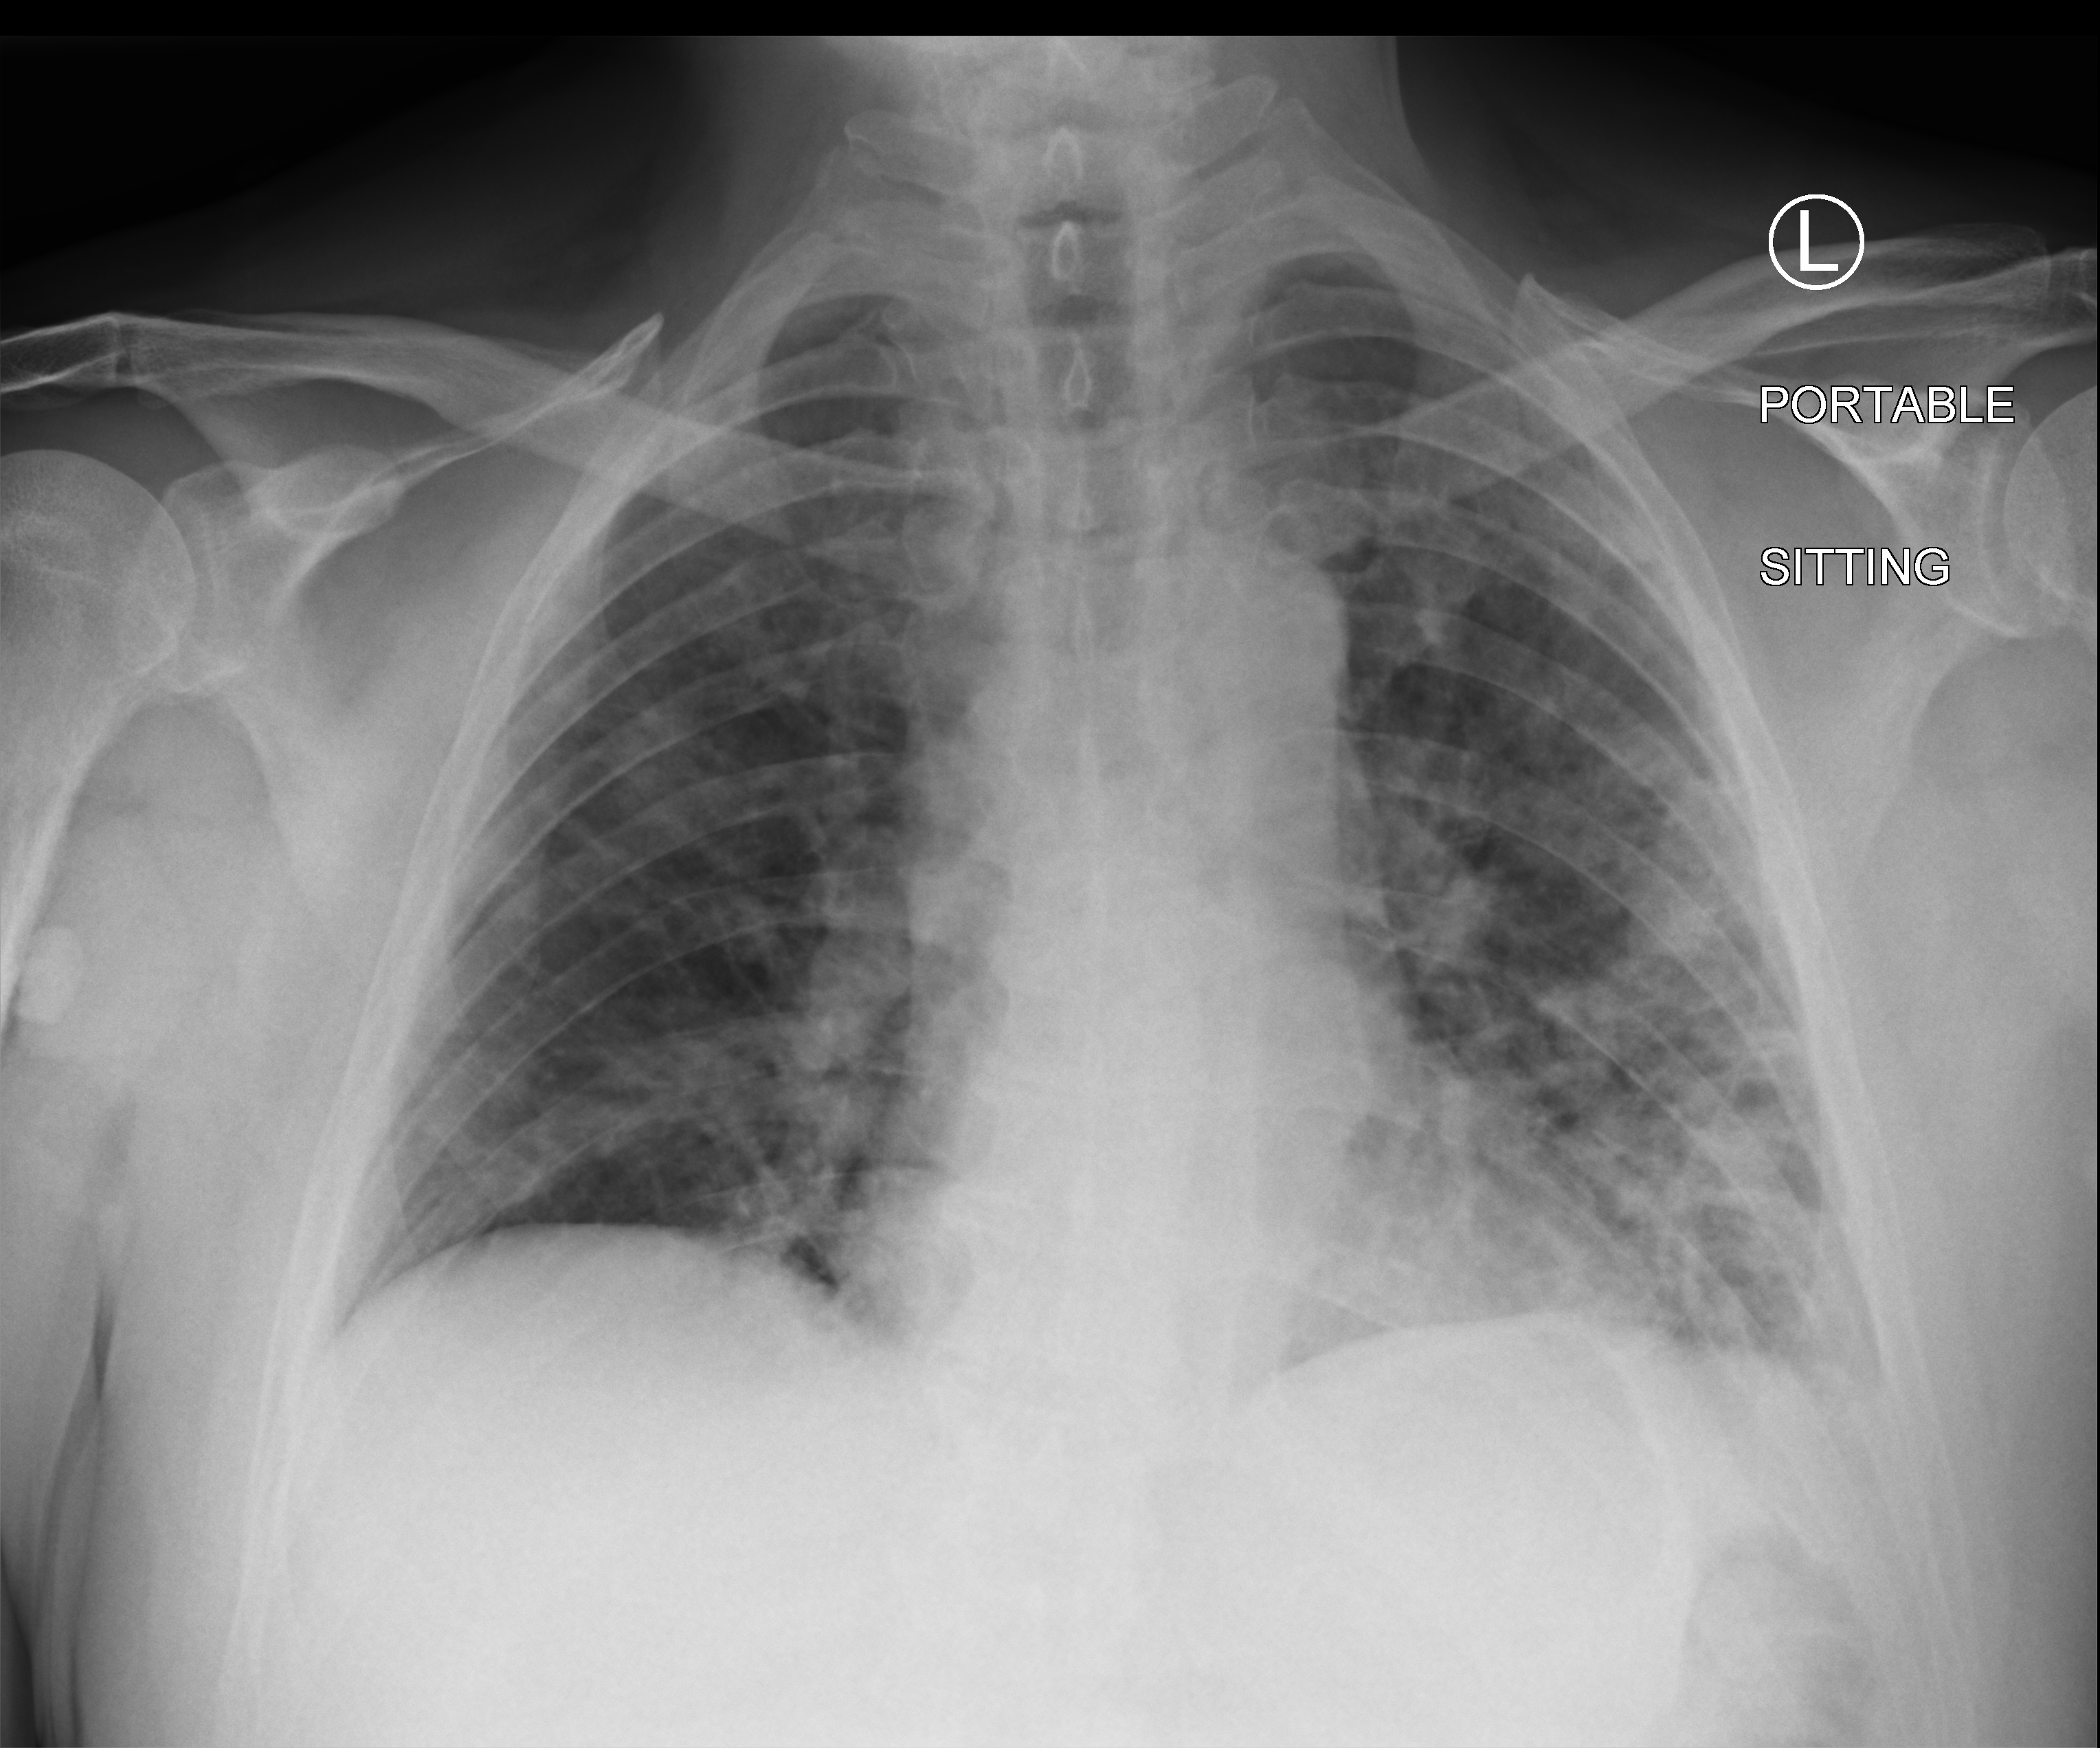
Chest X-ray (portable). Patient hospitalised with COVID-19; male, aged 18–59 years.
From the hospital-stay record, not from the radiograph (when in the stay this image was taken is not recorded):
- length of hospital stay: 1 day
- admitted to intensive care during this hospital stay: no
- mechanically ventilated during this hospital stay: no